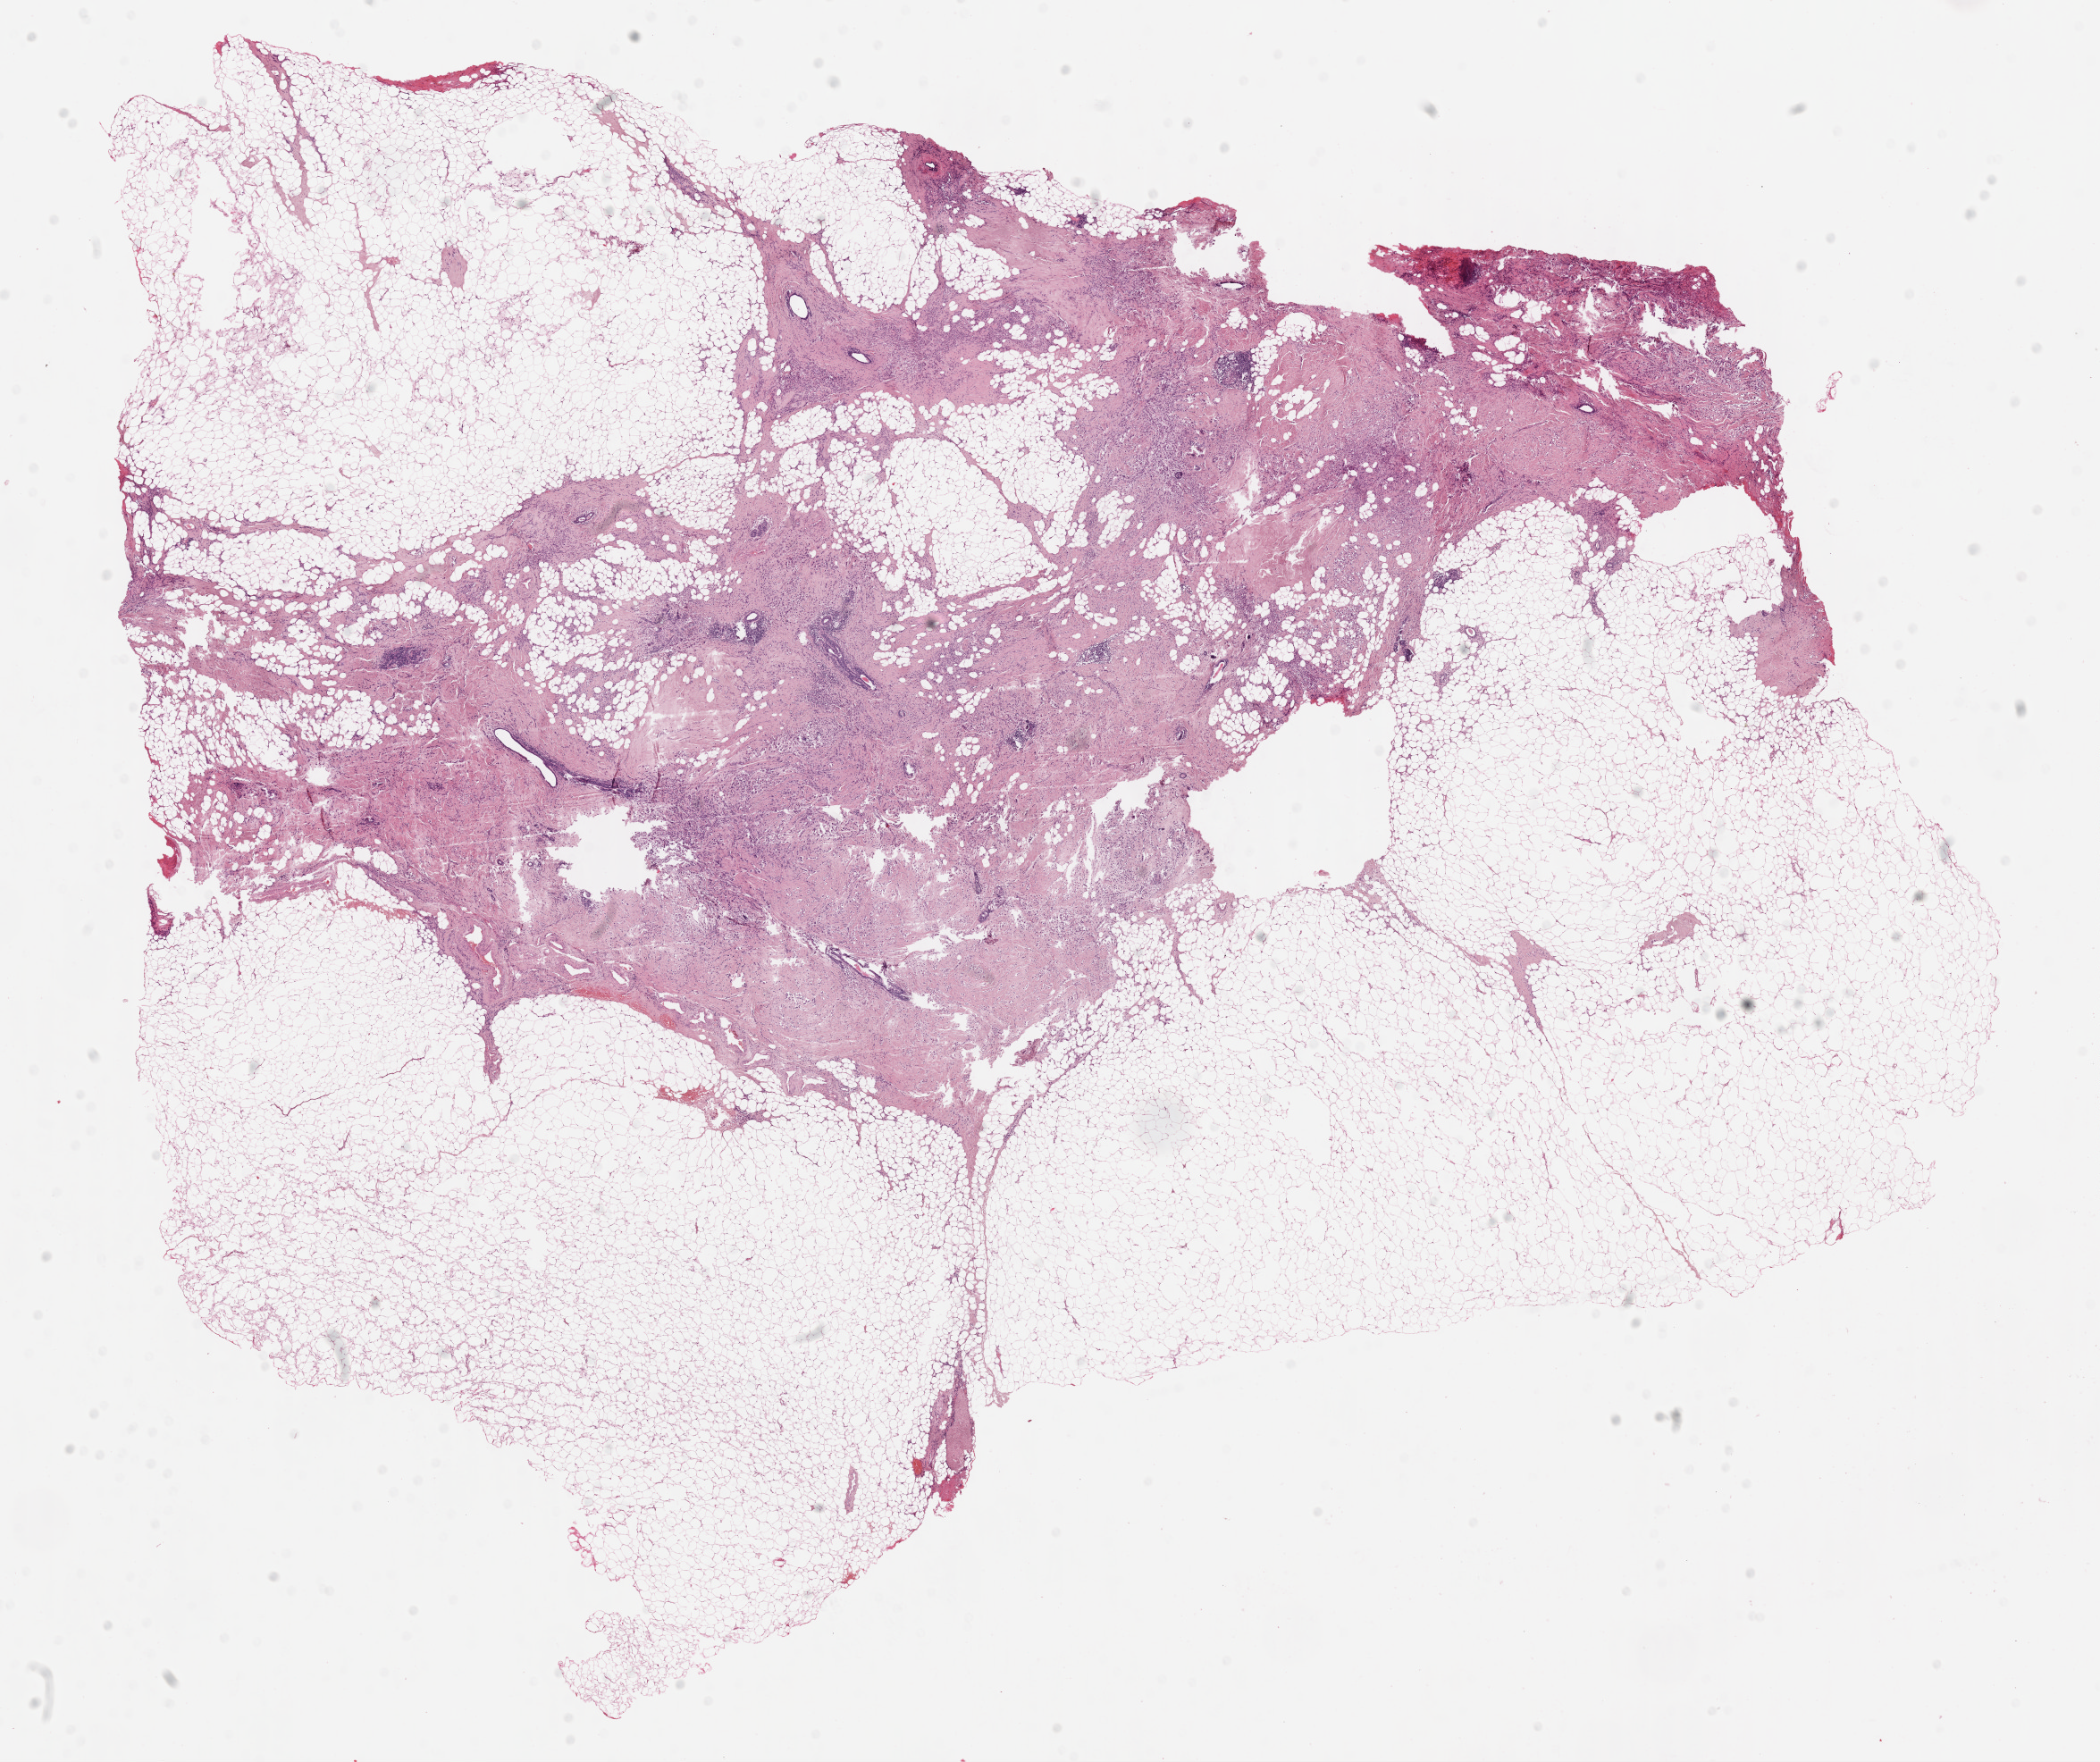
Whole-slide histology image, H&E-stained, whole scanned area (about 18.6 x 15.6 mm) shown as a low-resolution overview. FFPE section. Sample: primary tumour, breast. Female, age 58 years at initial diagnosis.
- lymph nodes positive (case pathology): 4 of 10 examined
- laterality: right
- pathologic diagnosis: Lobular carcinoma, NOS
- AJCC pathologic stage: IIIA